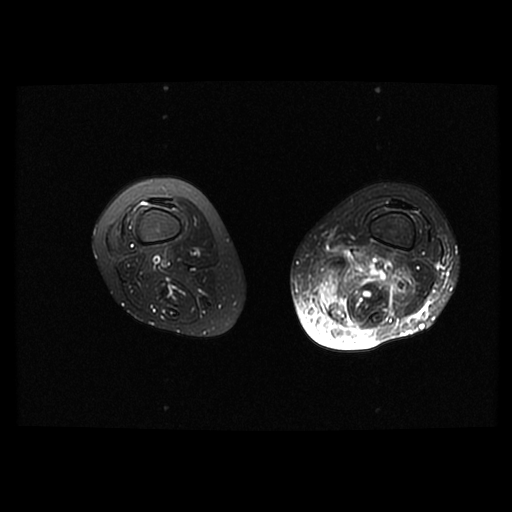
MRI of an extremity soft-tissue mass, one axial slice; slice 18 of 42 in the series (ordered by position); T2-weighted fat-saturated; 6 mm slice thickness; 512 × 512 image matrix. Female patient. From the clinical record (not read from this slice): histological type: pleomorphic leiomyosarcoma; grade: high; site of the primary tumour: left thigh.
Structures marked on this image (outlined manually by an expert reader):
- gross tumour volume including surrounding oedema: box from (x=316, y=250) to (x=411, y=322) px